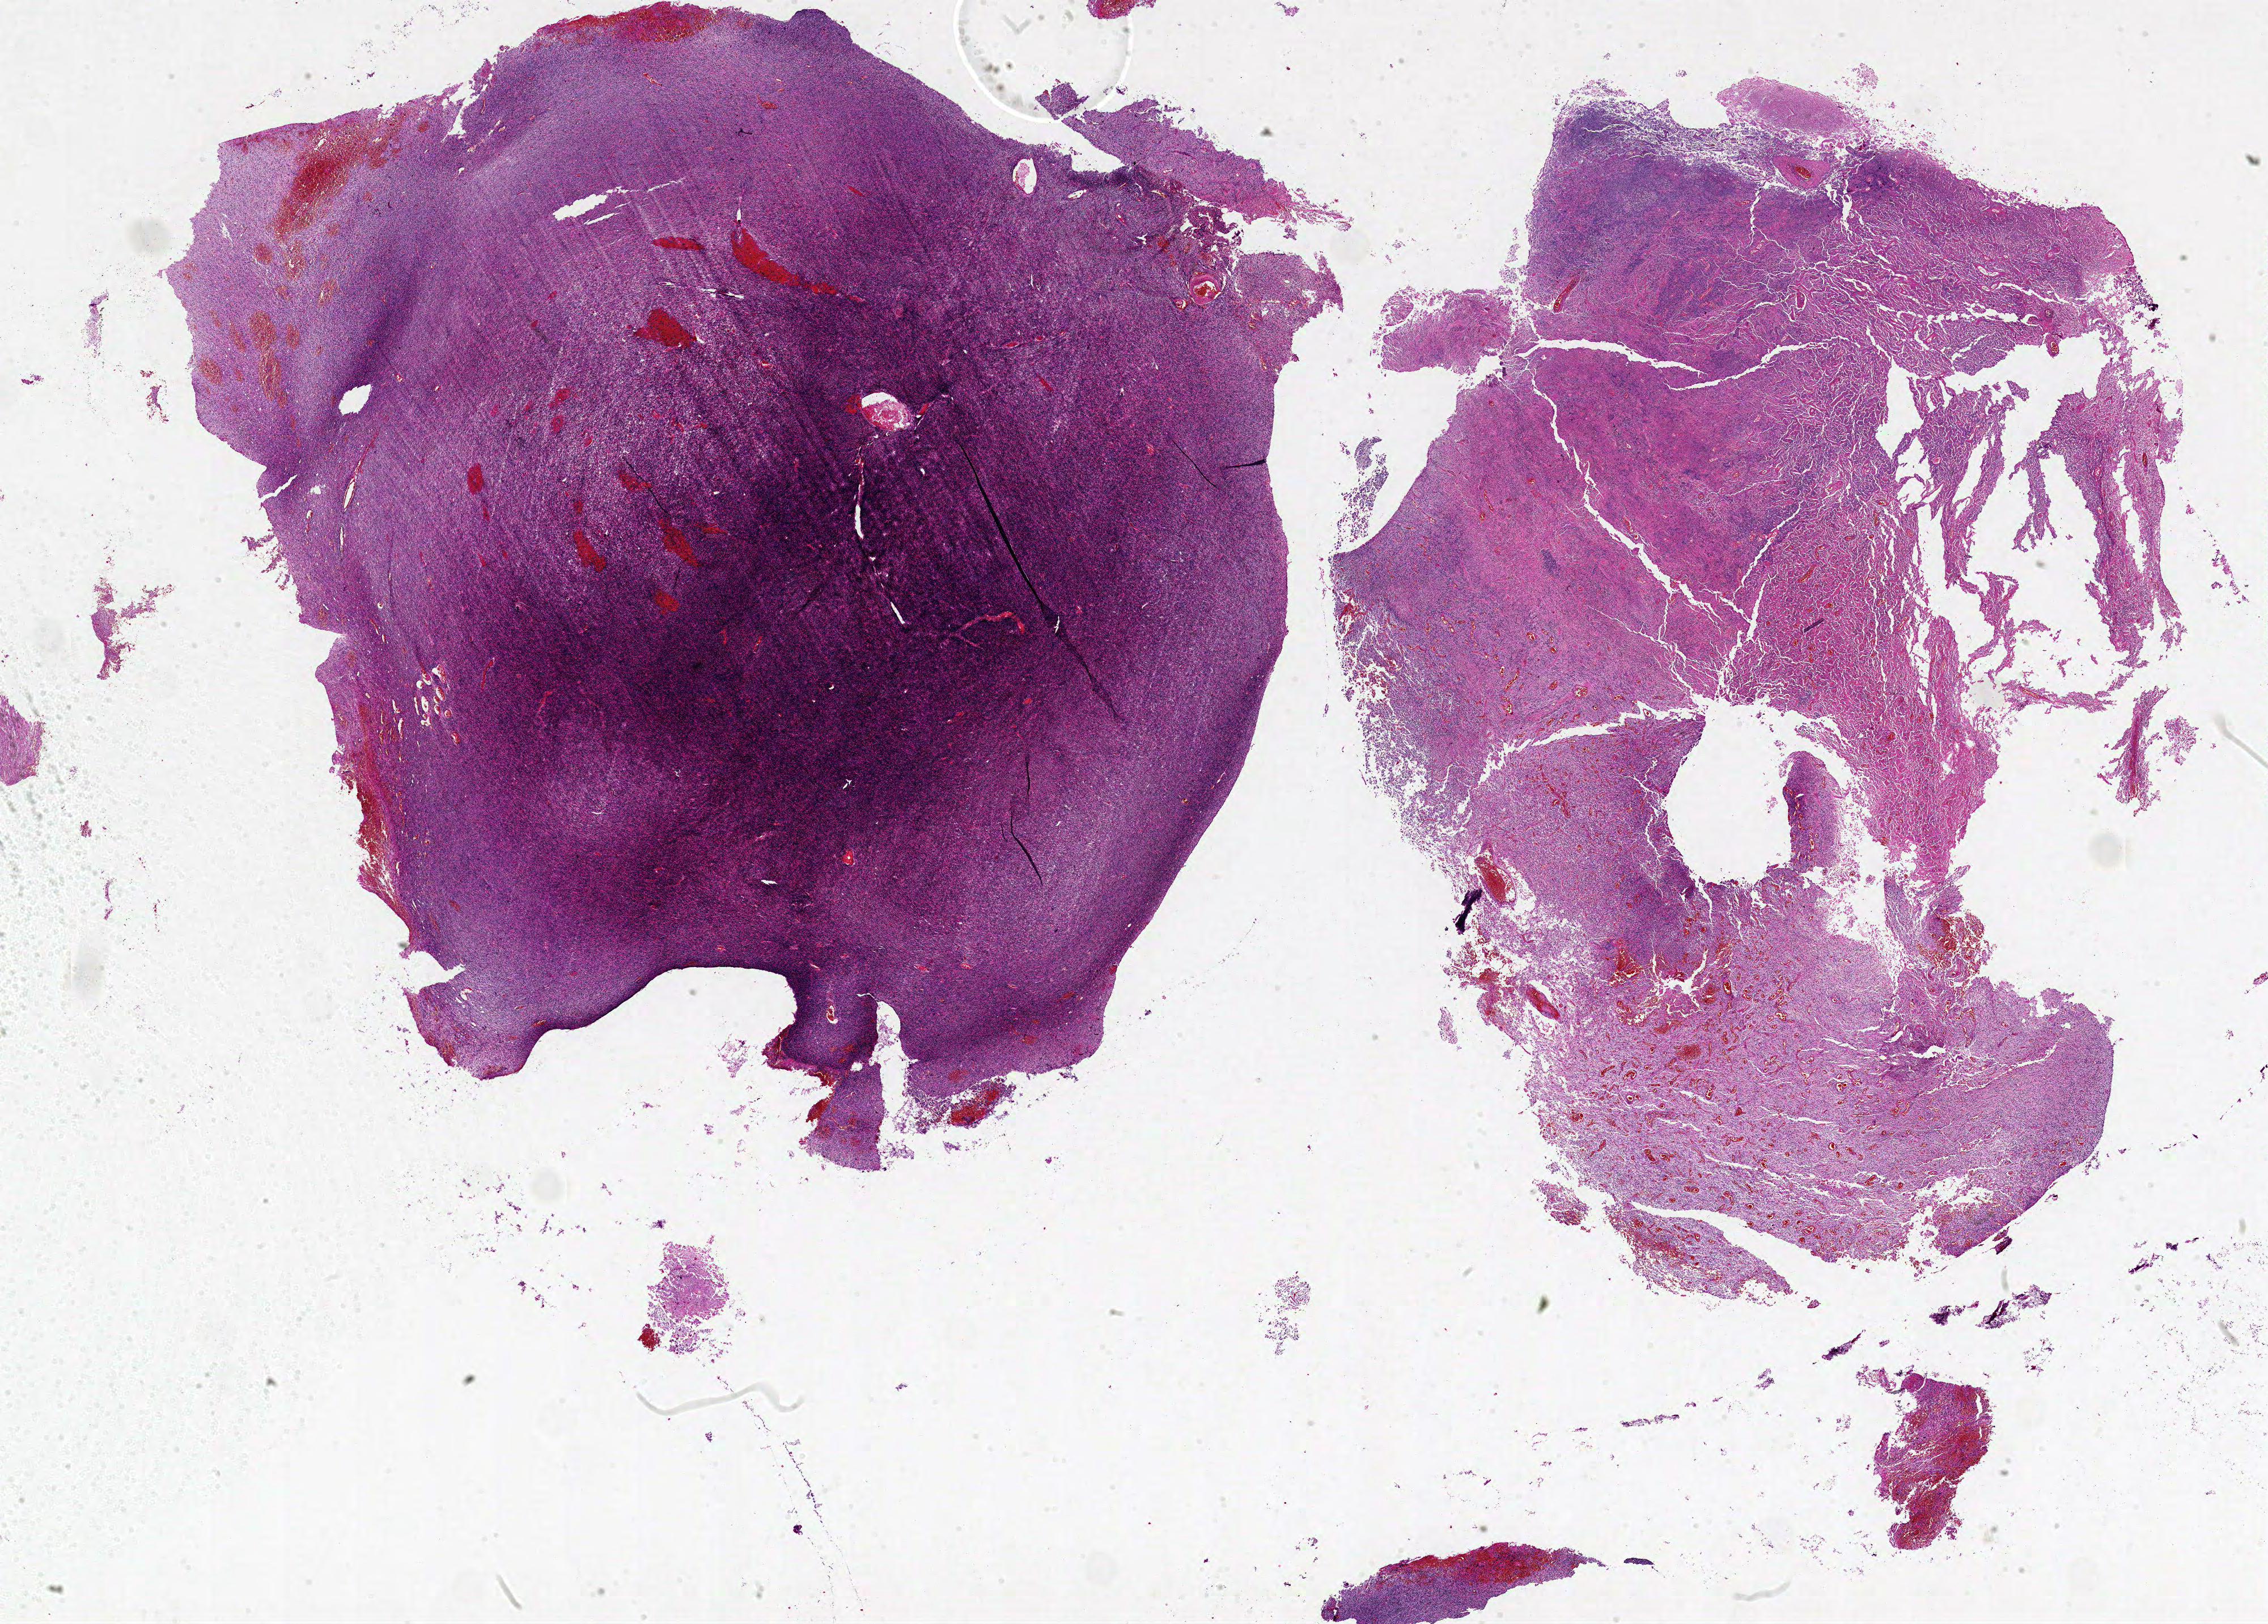
Digitized Hematoxylin and eosin (H&E) stained tissue section (whole slide), shown as a low-resolution overview of the whole scanned area (about 32.0 x 22.9 mm, from a 20x scan); formalin-fixed paraffin-embedded (FFPE) diagnostic section; brain, primary tumour sample. Female, age 61 years at initial diagnosis.
- histologic diagnosis: Glioblastoma